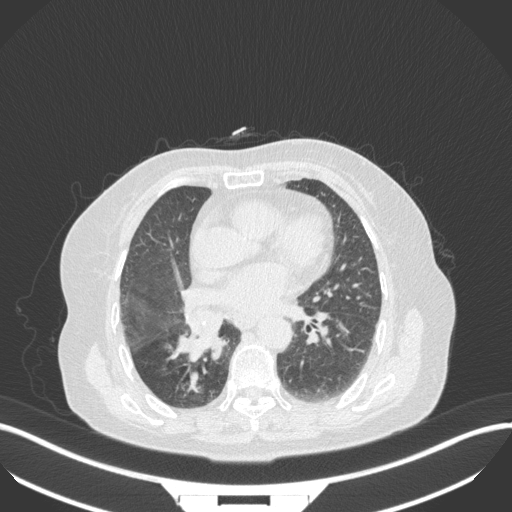
Chest CT, one axial slice; position 147 of 329 along the scan axis; reconstruction kernel B31f; 120 kVp; lung window (W 1500 / L -600 HU); 512 × 512 image matrix, field of view 400 × 400 mm. Patient: female, 75 years. From the clinical record (not read from this slice): clinical TNM (as recorded): T1b N0 M1a; histopathological grade: G1.
Annotated regions visible in this slice (rectangle marked by the reading radiologist):
- lung tumour (recorded histology: squamous cell carcinoma): box from (x=170, y=313) to (x=225, y=359) px